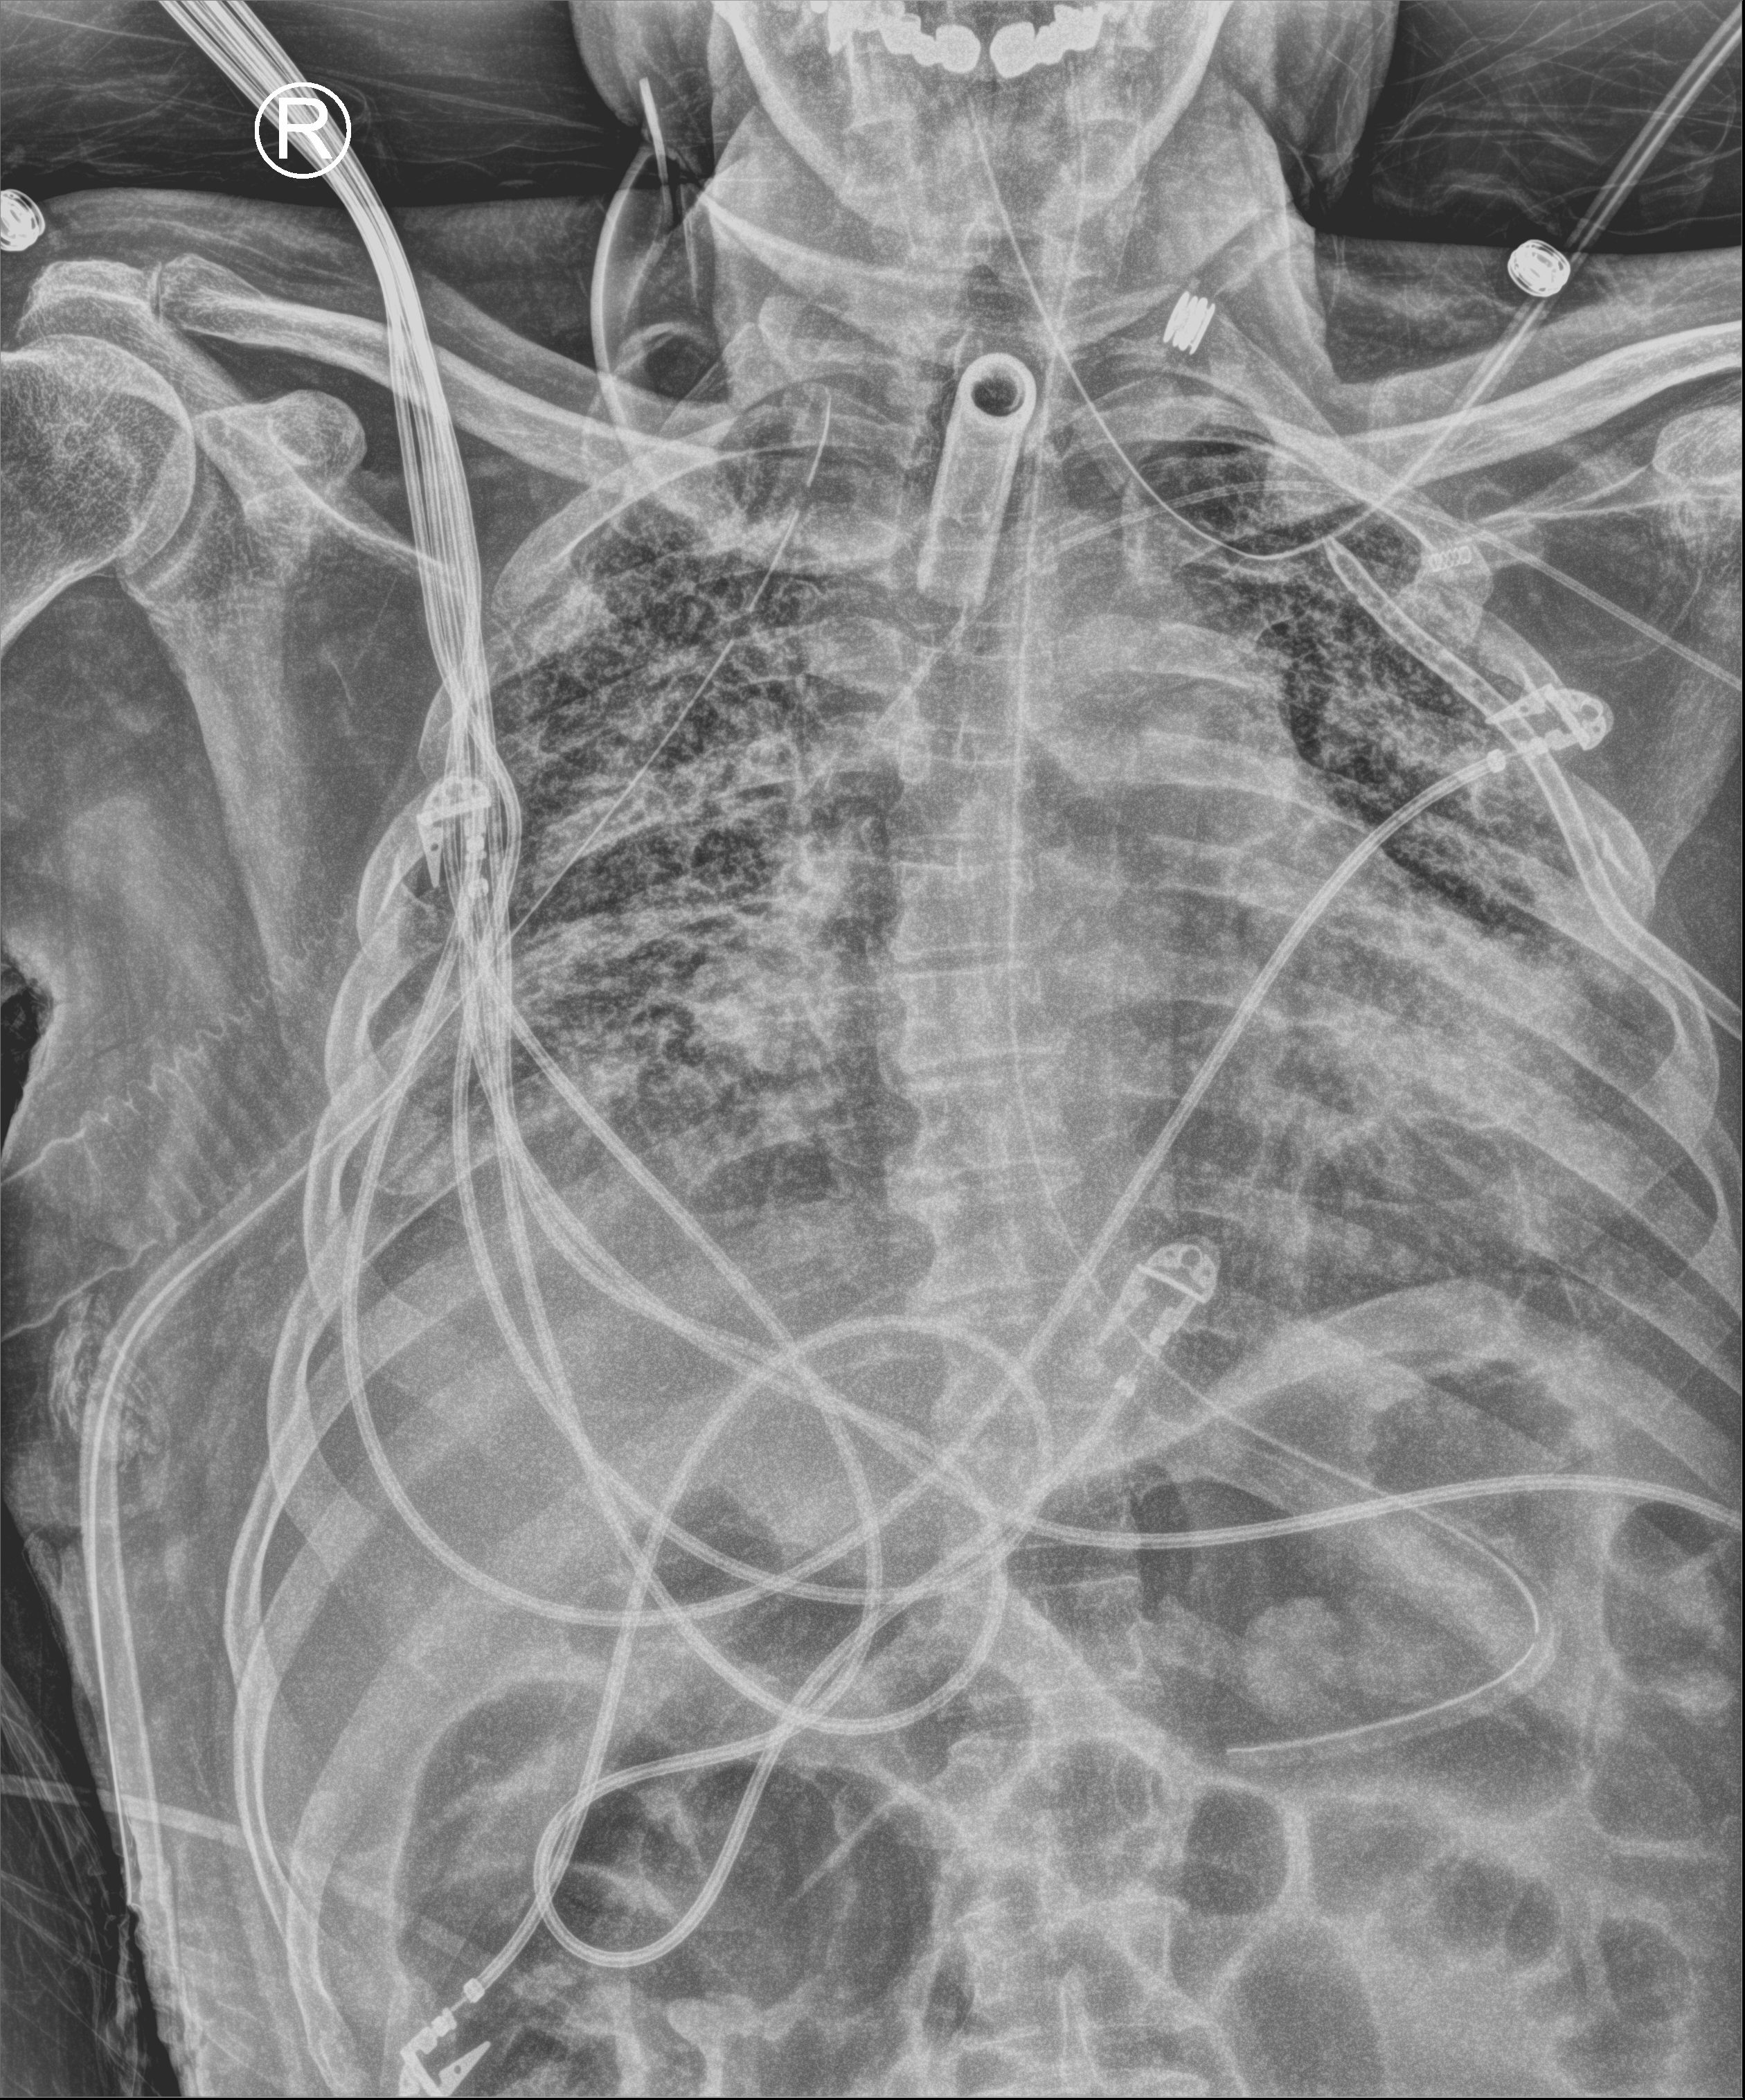
Chest X-ray (portable). Male patient hospitalised with COVID-19, age 18–59 years.
From the hospital-stay record, not from the radiograph (when in the stay this image was taken is not recorded): hypertension (admission record): yes; mechanically ventilated during this hospital stay: yes; diabetes (admission record): no.